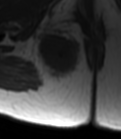
MRI of an extremity soft-tissue mass, one axial slice; position 27 of 47 along the scan axis; MR volume resampled by the dataset authors to the PET/CT grid (not the native acquisition matrix); 3.27 mm slice thickness; 121 × 139 image matrix, field of view 118 × 136 mm. Female patient. Case-level facts recorded for this patient, not image findings: histological type: epithelioid sarcoma; grade: intermediate; site of the primary tumour: right buttock.
Annotated regions visible in this slice (expert contour drawn on MRI and transferred to this co-registered scan by the dataset authors):
- gross tumour volume including surrounding oedema: box from (x=32, y=25) to (x=83, y=83) px
- gross tumour volume (mass): (x=36, y=34)–(x=80, y=78)